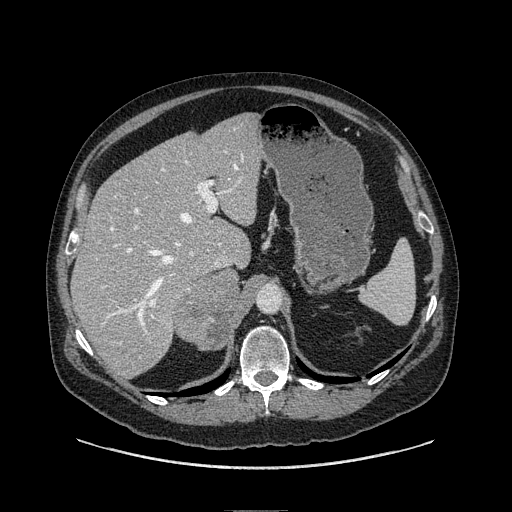
Contrast-enhanced abdominal CT, one axial slice; position 68 of 149 along the scan axis; soft-tissue window (W 400 / L 40 HU); 1.25 mm slice thickness; 512 × 512 image matrix, field of view 440 × 440 mm. Male patient. Case-level facts recorded for this patient, not image findings: diagnosis: adrenocortical carcinoma; tumour side: right adrenal; tumour size at pathology: 7.5 cm; Ki-67 index: 15 %; stage (as recorded): 2.
Annotated regions visible in this slice (semi-automatic segmentation, software-assisted and operator-edited):
- mass: bounding box (x1, y1, x2, y2) in pixels: (177, 272, 240, 344)